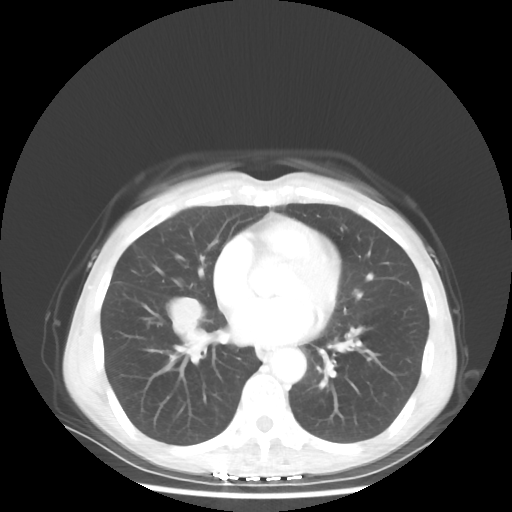
Chest CT, one axial slice. Slice 23 of 56 in the series (ordered by position). Reconstruction kernel STANDARD. Lung window (W 1500 / L -600 HU). 512 × 512 image matrix, field of view 360 × 360 mm. Patient: female, 57 years. Case-level facts recorded for this patient, not image findings: clinical TNM (as recorded): T1c N3 M1a; histopathological grade: G3.
Outlined on this slice (bounding box drawn by a radiologist):
- lung tumour (recorded histology: adenocarcinoma): bounding box (x1, y1, x2, y2) in pixels: (168, 292, 210, 342)